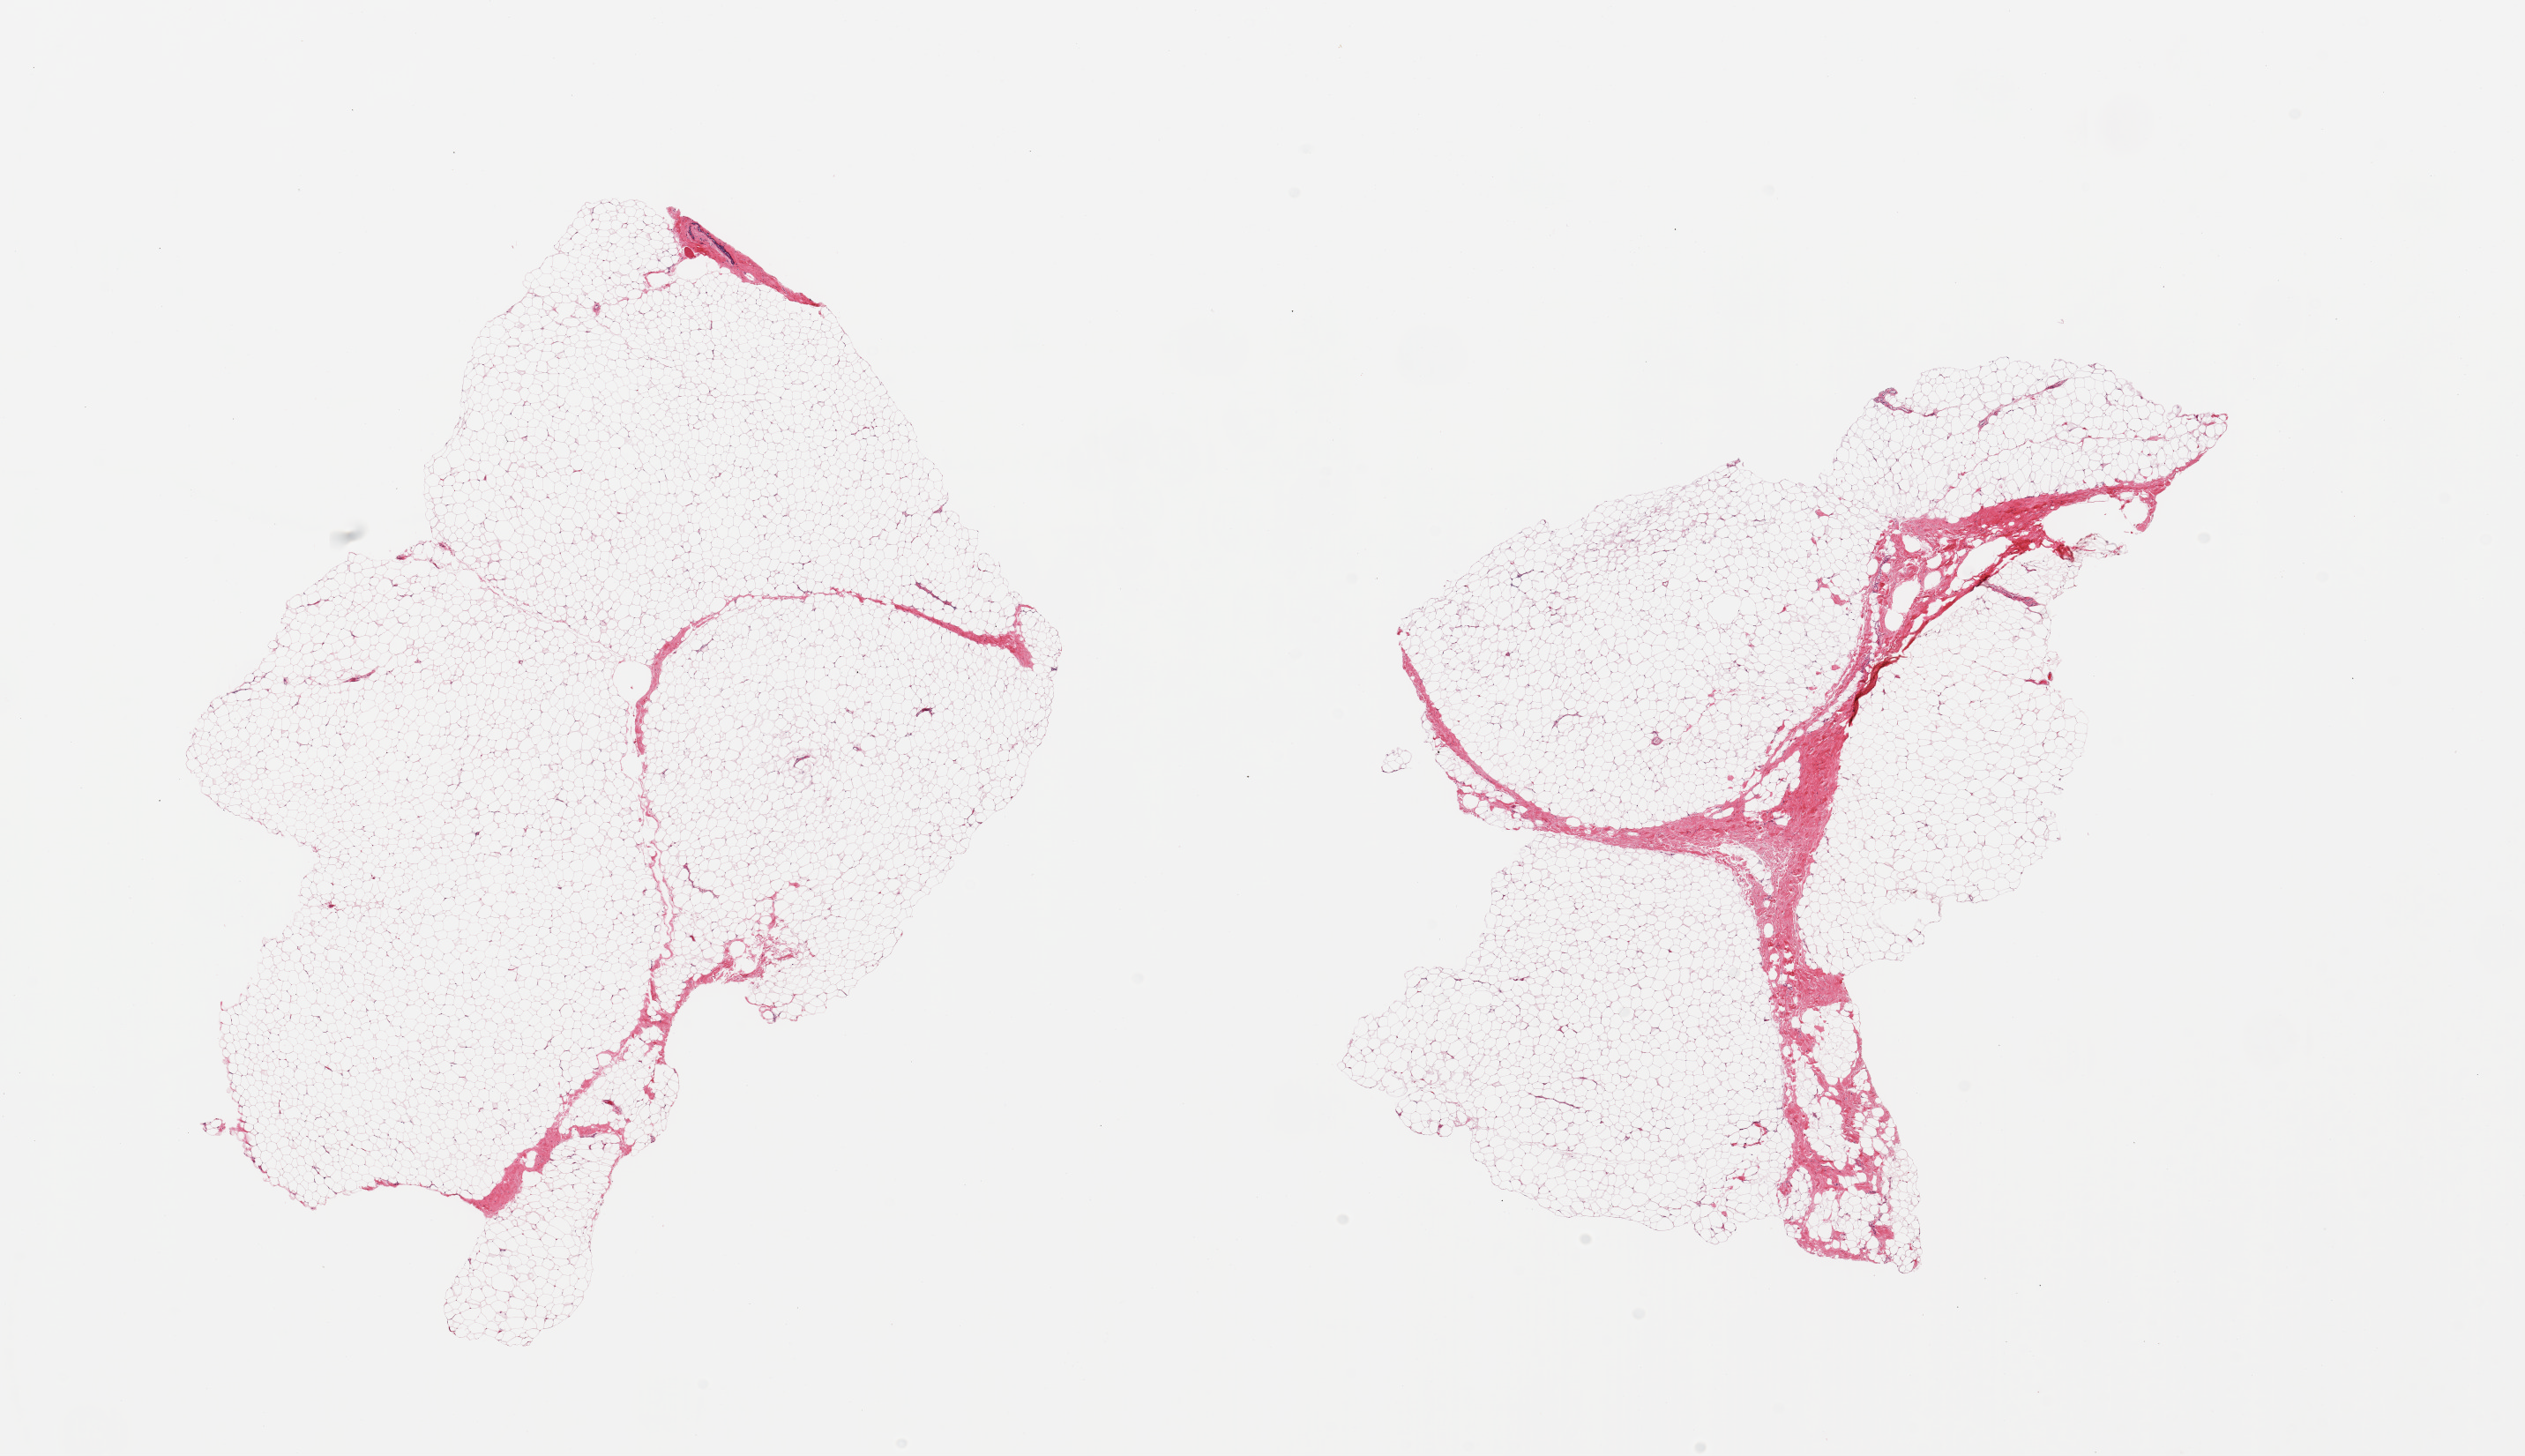
H&E whole-slide image — low-resolution overview of the scanned area, about 22.6 x 13.1 mm (acquisition: 20x scan); PAXgene-fixed, paraffin-embedded tissue; sampled site (target tissue): breast; donor tissue sample. Donor sex: male.
- reviewer comment on this tissue sample: 2 pieces, fibroadipose elements, no ductal elements noted